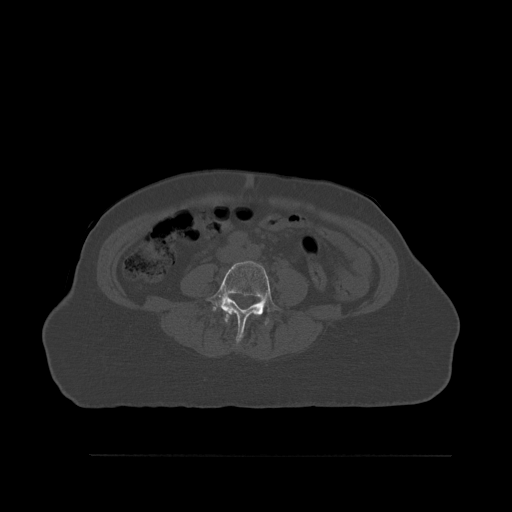
CT including the spine, one axial slice. Slice 207 of 527 in the series (ordered by position). Bone window (W 1800 / L 400 HU). 1.5 mm slice thickness. 512 × 512 image matrix, field of view 470 × 470 mm. Patient: female, 73 years. From the clinical record (not read from this slice): primary cancer: breast.
Structures marked on this image (semi-automatic segmentation, software-assisted and operator-edited):
- L3 vertebra: bounding box [x1, y1, x2, y2] px = [225, 309, 260, 323]
- L4 vertebra: [206, 261, 281, 342]
- L5 vertebra: [213, 306, 268, 324]